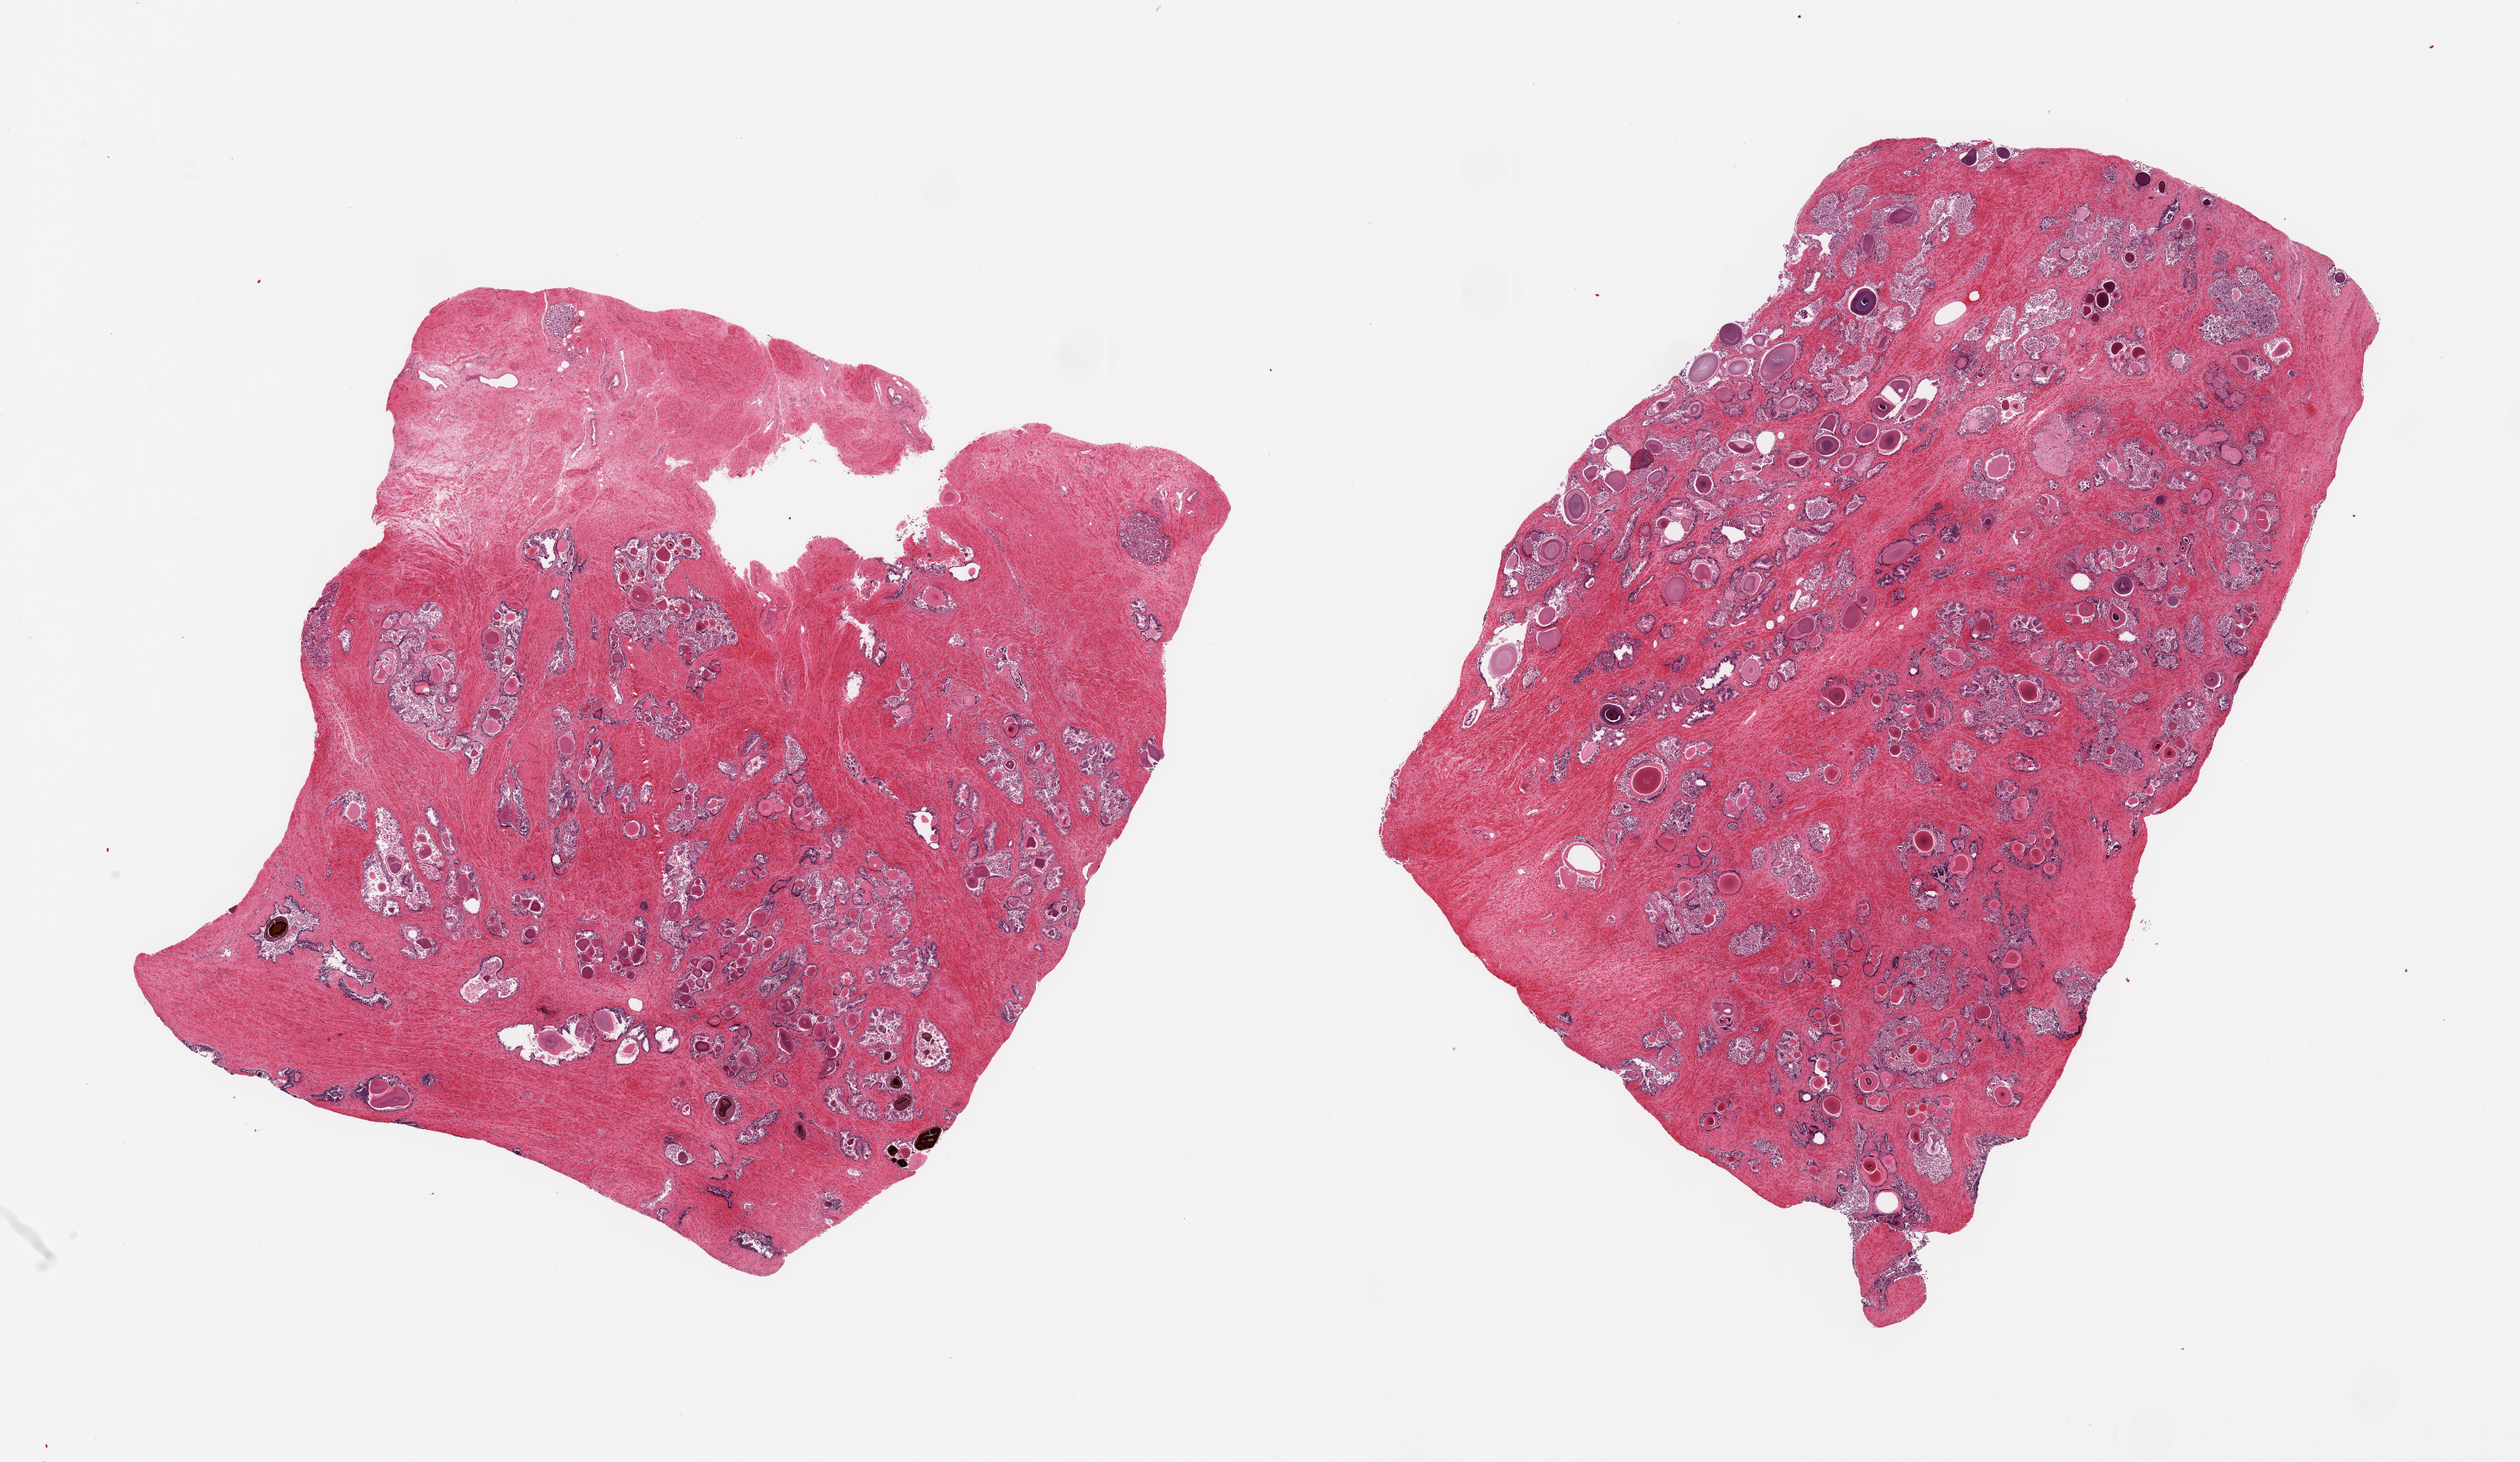
Whole-slide image, H&E stain, a low-resolution overview of the entire scanned area, about 24.6 x 14.3 mm (acquisition: 20x scan). PAXgene-fixed, paraffin-embedded tissue. Section of prostate (target tissue). Donor tissue sample. Donor sex: male.
Reviewer comment on this tissue sample: 2 pieces, glandular elements with moderately advanced autolysis.